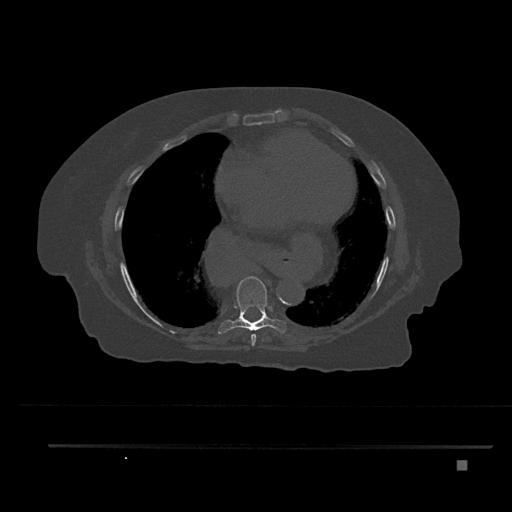
CT including the spine, one axial slice. Reconstruction kernel Br40s/3. Bone window (W 1800 / L 400 HU). 0.5 mm slice thickness. 512 × 512 image matrix, field of view 437 × 437 mm. Patient: female, 76 years. Case-level facts recorded for this patient, not image findings: primary cancer: lung; vertebrae with lytic lesions (as recorded): T11, L3.
Structures marked on this image (semi-automatic segmentation, software-assisted and operator-edited):
- T7 vertebra: box from (x=251, y=333) to (x=256, y=346) px
- T8 vertebra: (x=218, y=276)–(x=286, y=334)